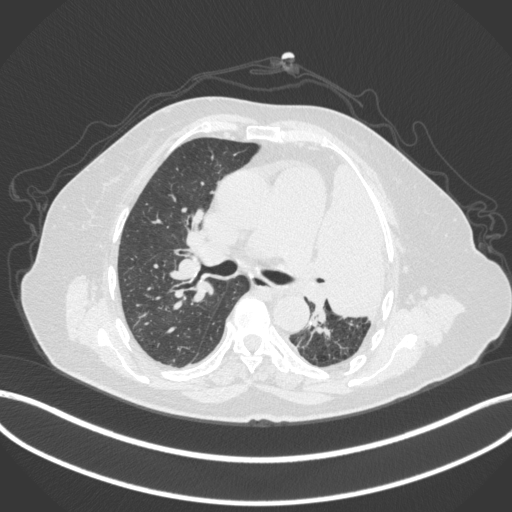
Chest CT, one axial slice; slice 238 of 399 in the series (ordered by position); 120 kVp; lung window (W 1500 / L -600 HU); 512 × 512 image matrix. Female patient, age 75 years. From the clinical record (not read from this slice): clinical TNM (as recorded): T3 N3 M1.
Annotated regions visible in this slice (bounding box drawn by a radiologist):
- lung tumour (recorded histology: adenocarcinoma): box from (x=315, y=158) to (x=393, y=326) px